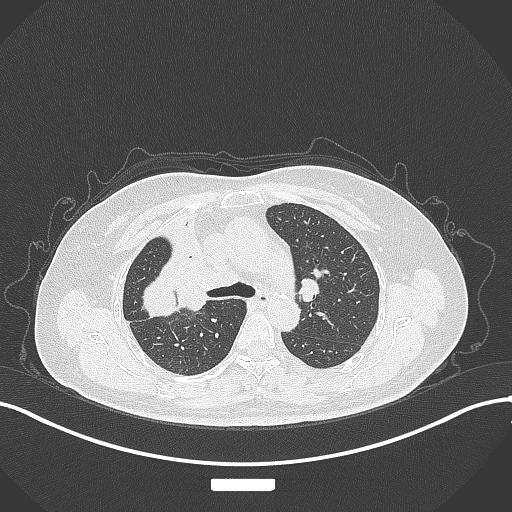
Chest CT, one axial slice. Slice 211 of 309 in the series (ordered by position). Reconstruction kernel B70f. Lung window (W 1500 / L -600 HU). 1 mm slice thickness. 512 × 512 image matrix, field of view 400 × 400 mm. Patient: female, 60 years. From the clinical record (not read from this slice): clinical TNM (as recorded): T3 N1 M1.
Structures marked on this image (rectangle marked by the reading radiologist):
- lung tumour (recorded histology: adenocarcinoma): bounding box (x1, y1, x2, y2) in pixels: (132, 266, 185, 324)